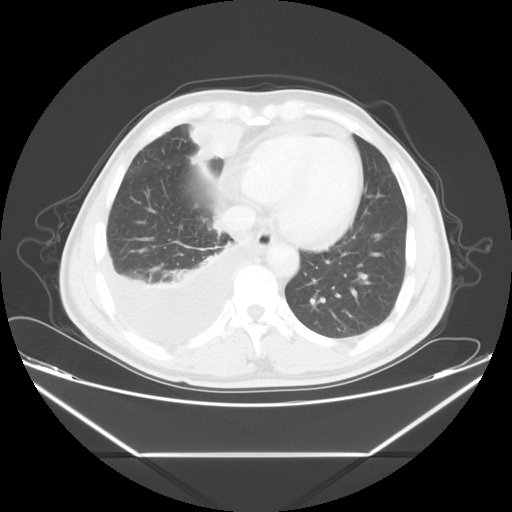
Chest CT, one axial slice. Slice 15 of 56 in the series (ordered by position). Reconstruction kernel STANDARD. Lung window (W 1500 / L -600 HU). 5 mm slice thickness. 512 × 512 image matrix. Male patient, age 57 years. From the clinical record (not read from this slice): clinical TNM (as recorded): T2 N3 M1.
Outlined on this slice (bounding box drawn by a radiologist):
- lung tumour (recorded histology: adenocarcinoma): bounding box [x1, y1, x2, y2] px = [190, 115, 245, 162]